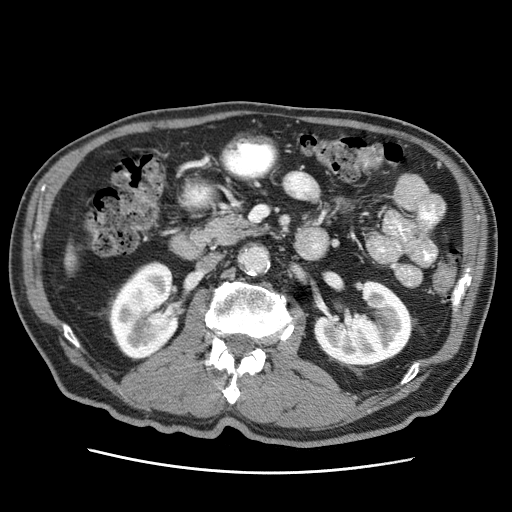
Contrast-enhanced abdominal CT (liver protocol), one axial slice. Position 5 of 75 along the scan axis. Soft-tissue window (W 400 / L 40 HU). 512 × 512 image matrix, field of view 360 × 360 mm. From the clinical record (not read from this slice): diagnosis: hepatocellular carcinoma (patient treated with transarterial chemoembolisation; whether this scan precedes or follows treatment is not stated here); TNM stage (as recorded): Stage-IIIA; Child-Pugh class: A; tumour differentiation: well differentiated; tumour nodularity: multinodular.
Annotated regions visible in this slice (semi-automatically segmented with operator editing):
- liver parenchyma outside the tumour (the mass and vessels are separate outlines, so this box may not span the whole liver): box from (x=64, y=246) to (x=76, y=272) px